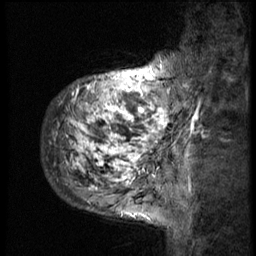
Breast MRI (dynamic contrast-enhanced), one sagittal slice; slice 10 of 58 in the series (ordered by position); 3 images stored at this slice position (order not interpretable as contrast timing); 1.5 T; TE 4.2 ms, TR 9 ms; 2.5 mm slice thickness; 256 × 256 image matrix. Female patient, age 50 years. From the clinical record (not read from this slice): setting: breast cancer imaged before/during neoadjuvant chemotherapy; receptor status: triple-negative.
Annotated regions visible in this slice (semi-automatic segmentation, software-assisted and operator-edited):
- analysis volume of interest (the breast-tissue region the enhancement analysis was run in; not a lesion): bounding box [x1, y1, x2, y2] px = [42, 48, 186, 214]
- tumour enhancement mask (voxels above the 140 % enhancement threshold inside the analysis volume of interest): [54, 69, 173, 190]